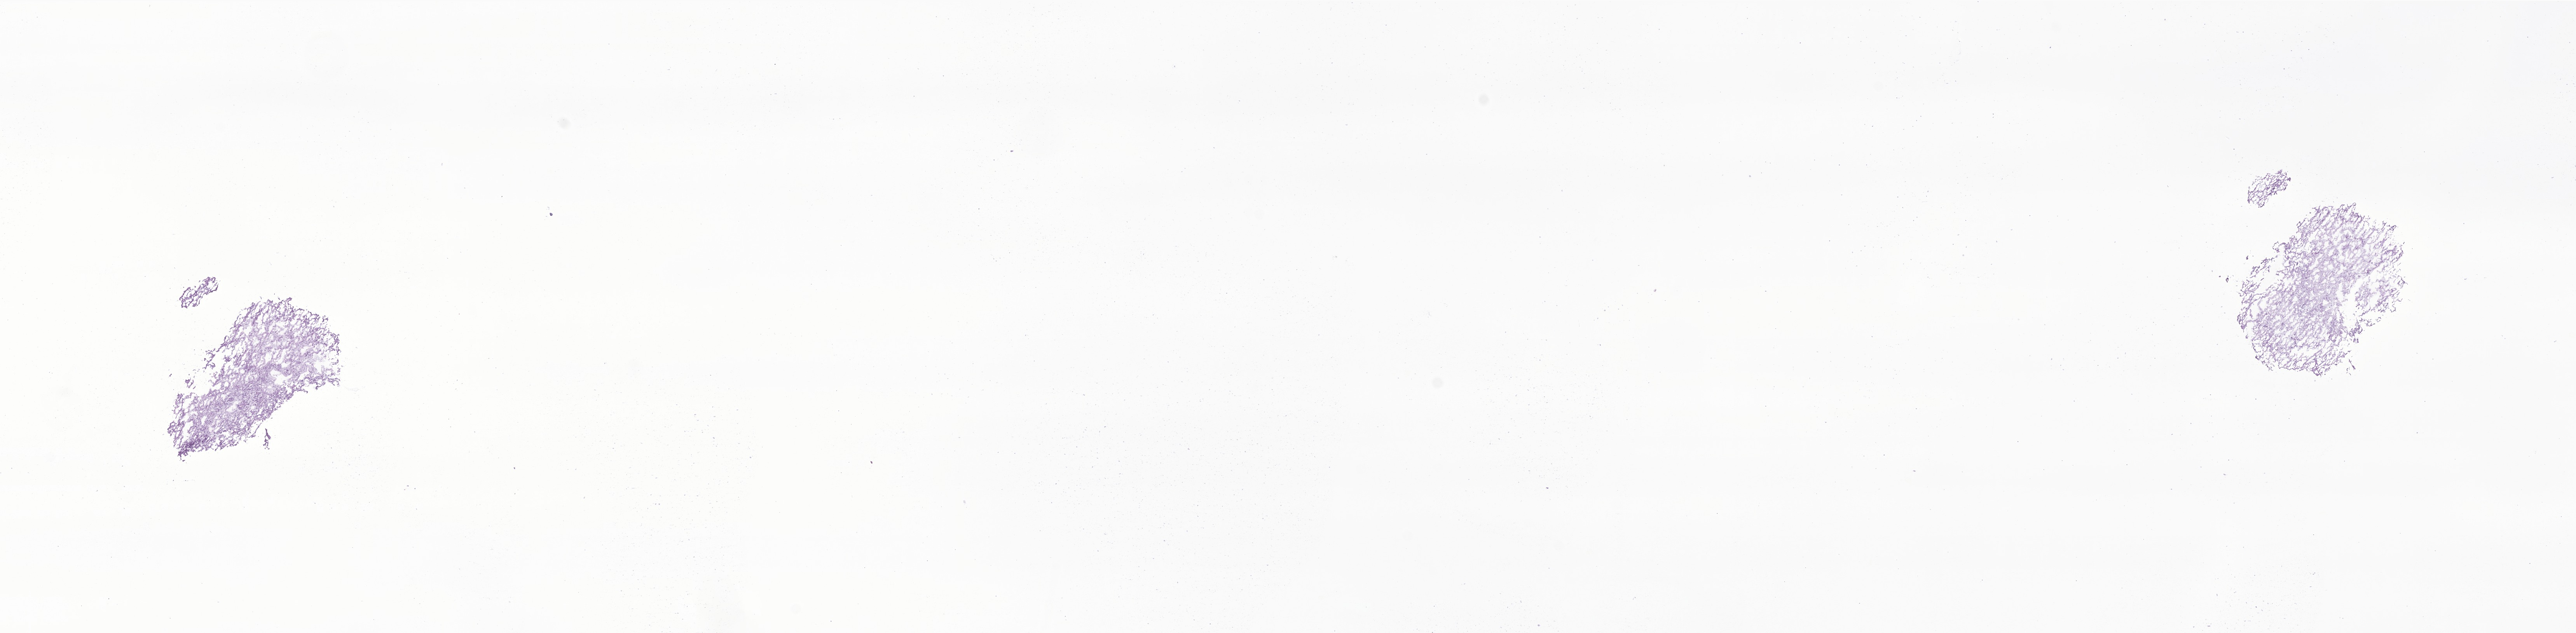
Hematoxylin and eosin (H&E) whole-slide image of tumor tissue from the brain — whole scanned area (about 27.9 x 6.9 mm) shown as a low-resolution overview. Frozen section. Male patient, age 81 months (6 years 9 months).
Diagnosis: Dysembryoplastic neuroepithelial tumor.